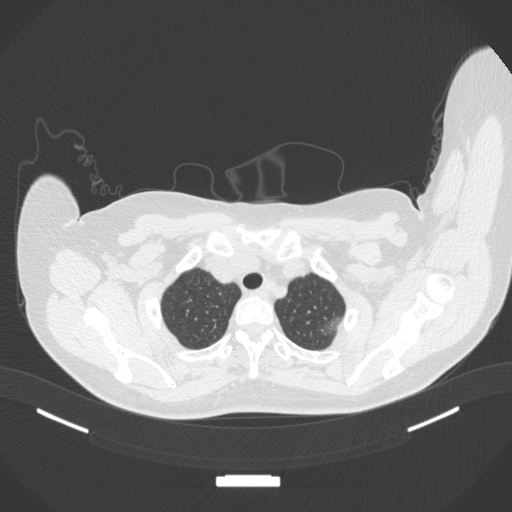
Chest CT, one axial slice. Position 326 of 386 along the scan axis. 120 kVp. Lung window (W 1500 / L -600 HU). 1 mm slice thickness. 512 × 512 image matrix, field of view 400 × 400 mm. Female patient, age 58 years. From the clinical record (not read from this slice): clinical TNM (as recorded): T1c N0 M0.
Structures marked on this image (bounding box drawn by a radiologist):
- lung tumour (recorded histology: adenocarcinoma): bounding box [x1, y1, x2, y2] px = [316, 314, 344, 336]